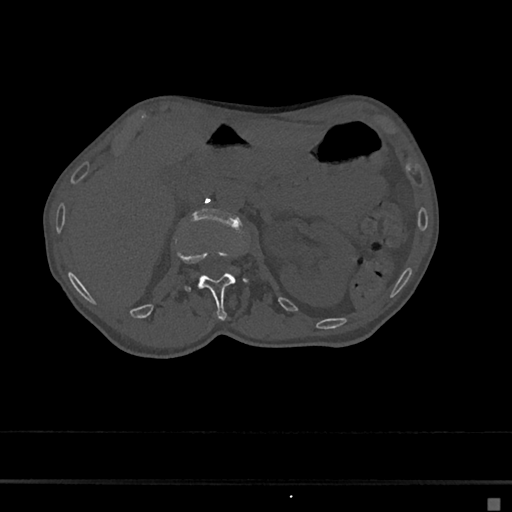
CT including the spine, one axial slice. Position 59 of 797 along the scan axis. Reconstruction kernel Br40s/3. 120 kVp. Bone window (W 1800 / L 400 HU). 512 × 512 image matrix, field of view 360 × 360 mm. Patient: female, 68 years. Case-level facts recorded for this patient, not image findings: primary cancer: renal.
Annotated regions visible in this slice (semi-automatically segmented with operator editing):
- L1 vertebra: bounding box (x1, y1, x2, y2) in pixels: (176, 249, 249, 320)
- L2 vertebra: (191, 208, 240, 226)